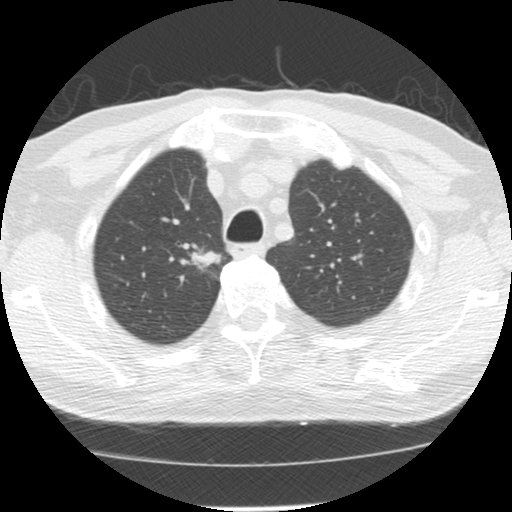
Low-dose screening chest CT, one axial slice; slice 107 of 139 in the series (ordered by position); reconstruction kernel STANDARD; 120 kVp; lung window (W 1500 / L -600 HU); 2.5 mm slice thickness; 512 × 512 image matrix, field of view 310 × 310 mm.
Structures marked on this image (outlined manually by an expert reader):
- lesion 1 (tumor, upper lobe of right lung): box from (x=191, y=249) to (x=222, y=271) px